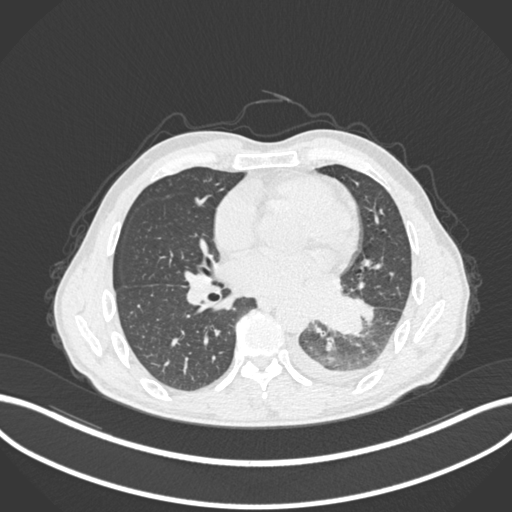
Chest CT, one axial slice. Position 110 of 222 along the scan axis. 120 kVp. Lung window (W 1500 / L -600 HU). 1 mm slice thickness. 512 × 512 image matrix, field of view 400 × 400 mm. Patient: male, 47 years. From the clinical record (not read from this slice): clinical TNM (as recorded): T3 N1 M1c; histopathological grade: G3.
Structures marked on this image (rectangle marked by the reading radiologist):
- lung tumour (recorded histology: small cell carcinoma): bounding box <315,295,362,342> (left, top, right, bottom; pixels)